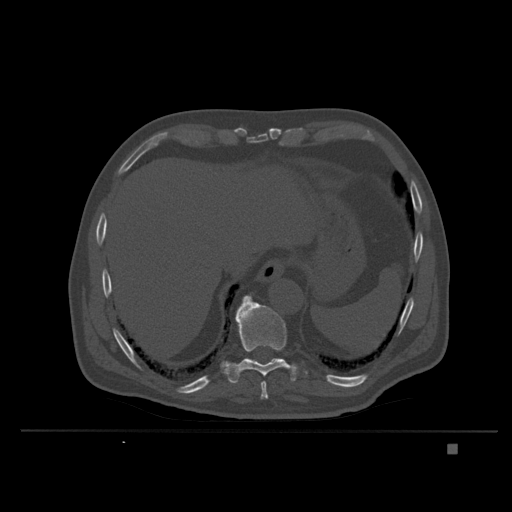
CT including the spine, one axial slice. Slice 195 of 435 in the series (ordered by position). Bone window (W 1800 / L 400 HU). 512 × 512 image matrix. Male patient, age 73 years. From the clinical record (not read from this slice): primary cancer: skin.
Structures marked on this image (semi-automatic segmentation, software-assisted and operator-edited):
- T10 vertebra: bounding box [x1, y1, x2, y2] px = [227, 296, 307, 384]
- T11 vertebra: [235, 295, 251, 318]
- T9 vertebra: [260, 381, 268, 401]